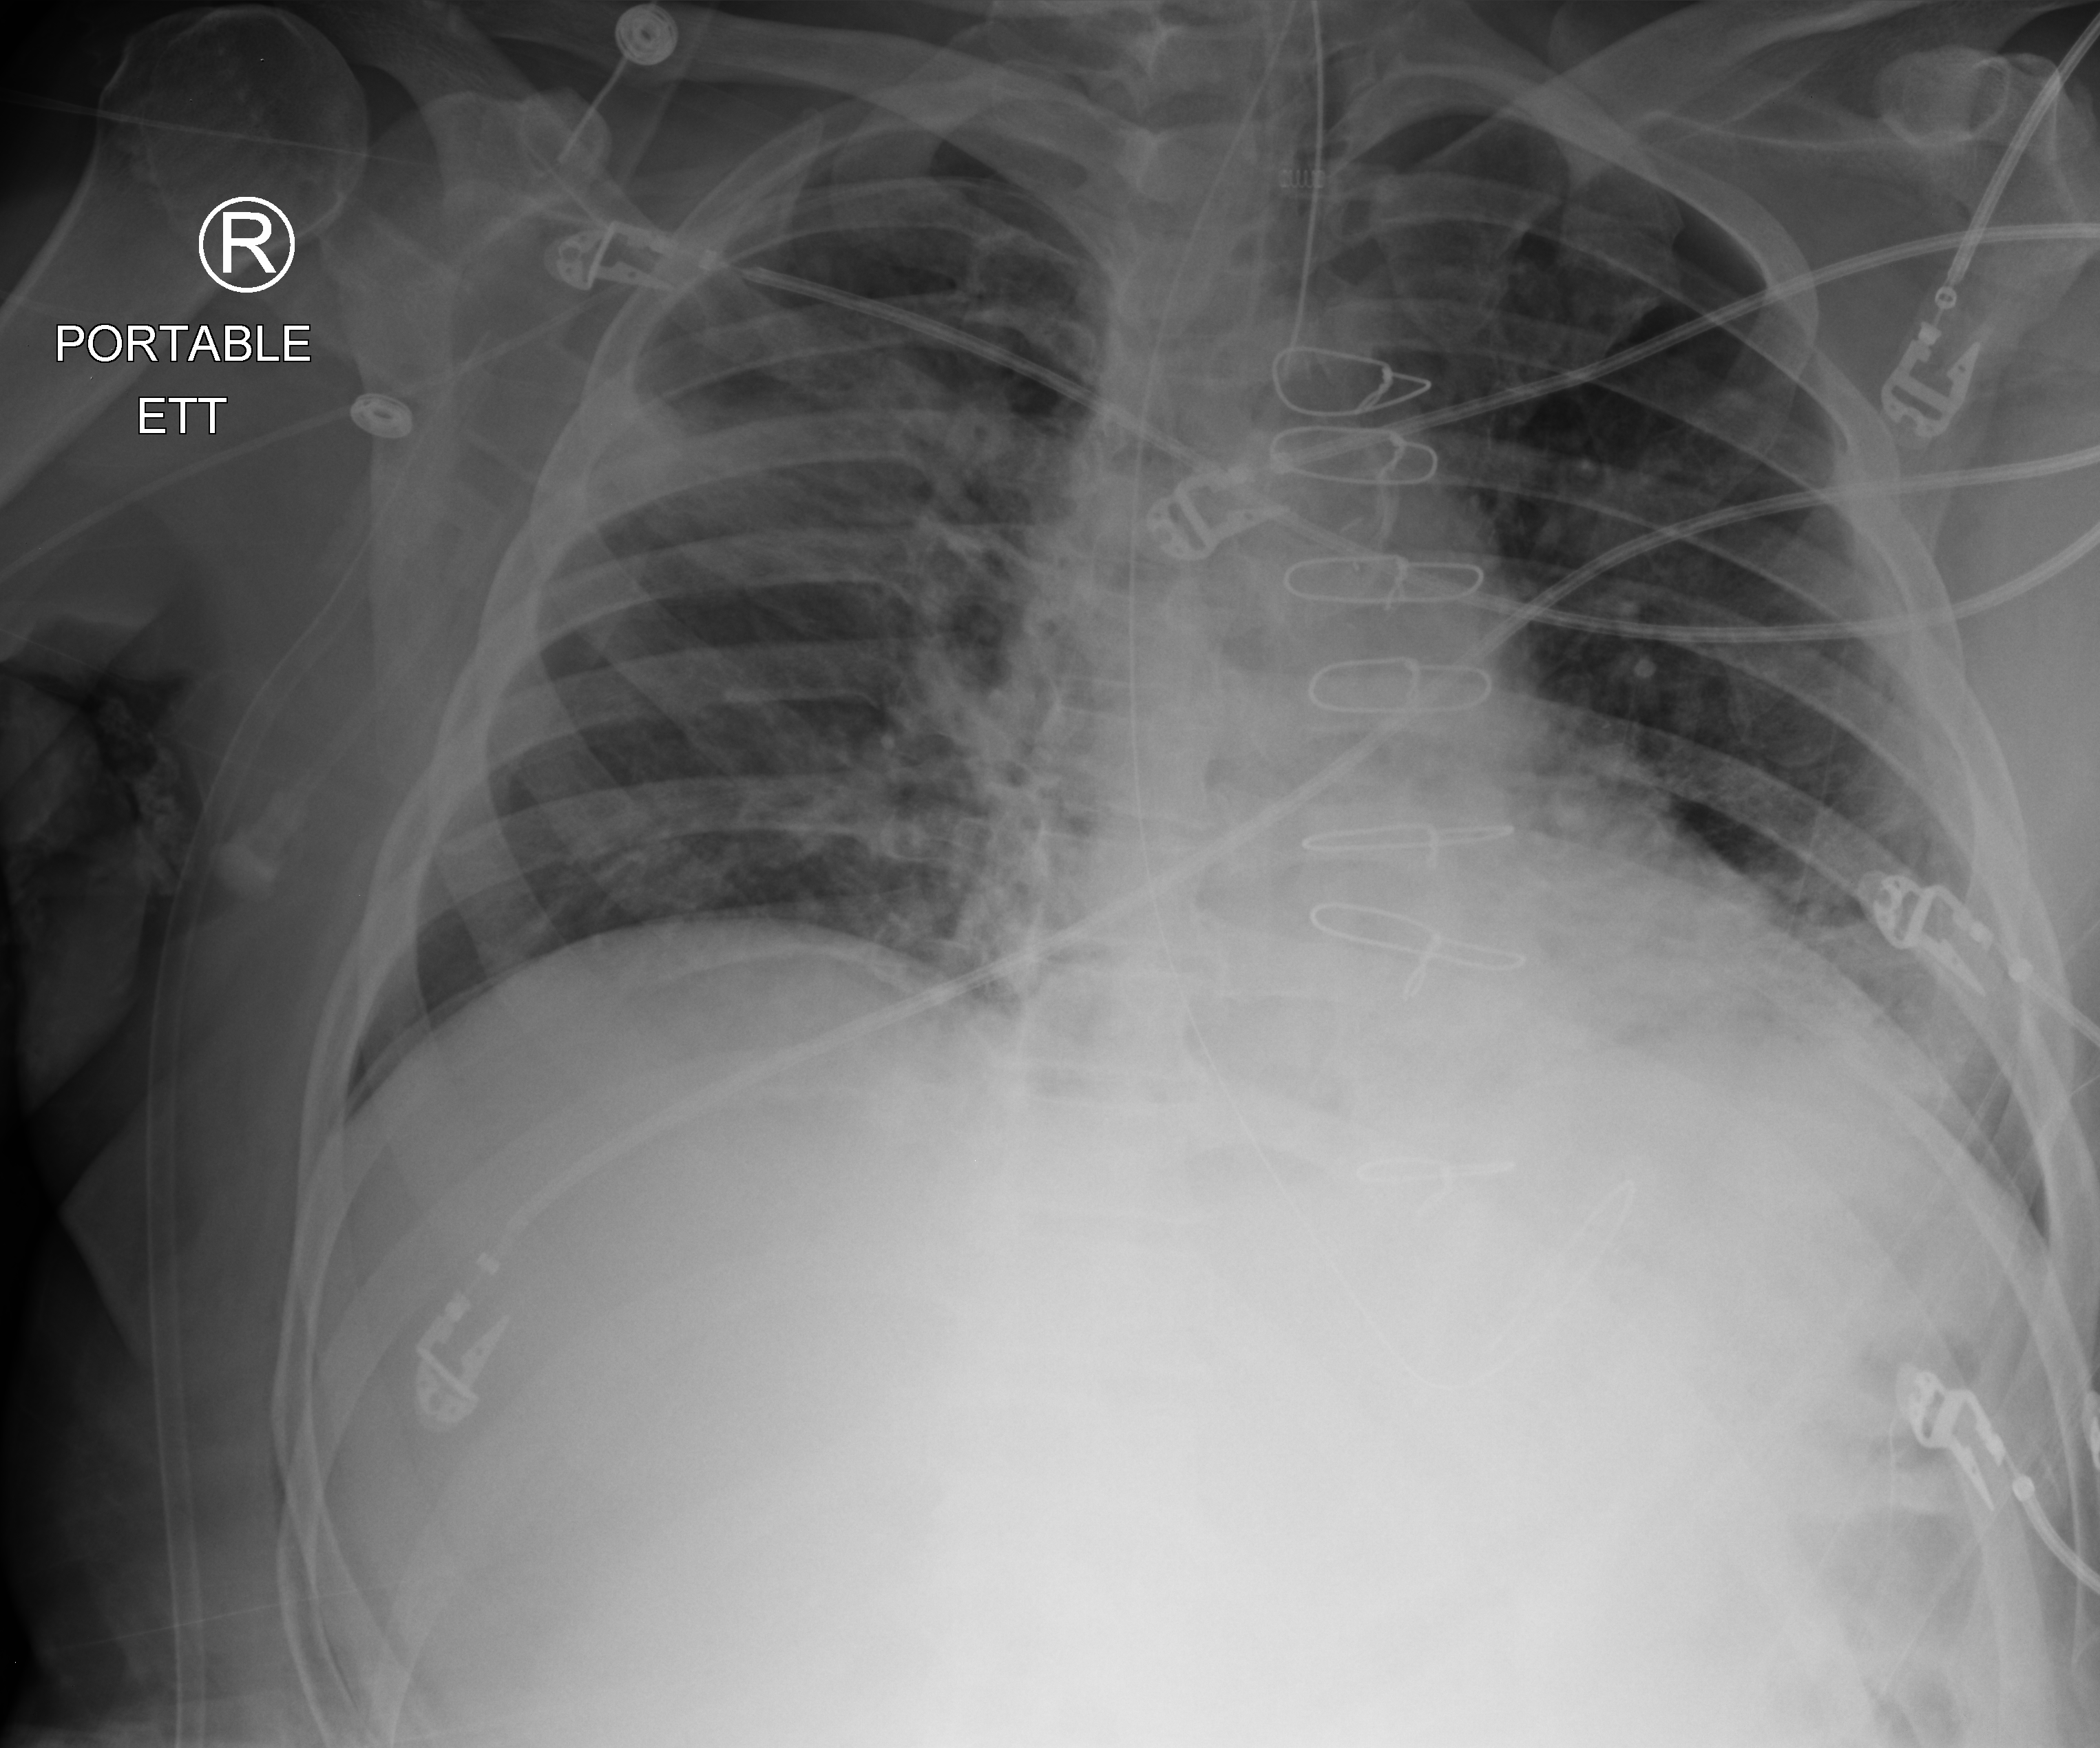
Chest X-ray (portable); anteroposterior (AP) projection. Male patient hospitalised with COVID-19, age 60–74 years.
Hospital-stay facts (about this admission, not read from this image; timing relative to this image not recorded): diabetes (admission record): yes; length of hospital stay: 44 days.